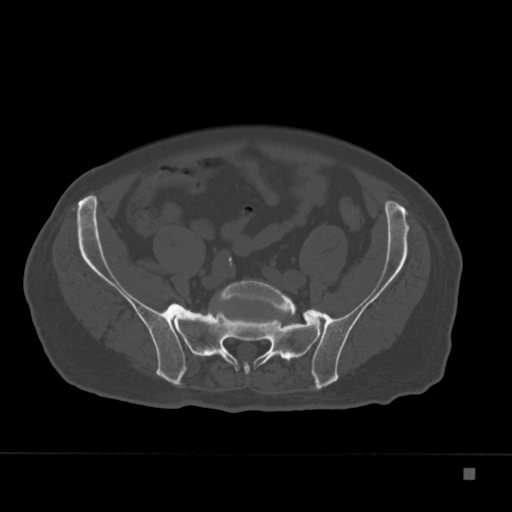
CT including the spine, one axial slice; position 9 of 332 along the scan axis; reconstruction kernel Br40s; 120 kVp; bone window (W 1800 / L 400 HU); 512 × 512 image matrix, field of view 389 × 389 mm. Patient: male, 72 years. From the clinical record (not read from this slice): primary cancer: skeletal.
Structures marked on this image (semi-automatically segmented with operator editing):
- L5 vertebra: bounding box (x1, y1, x2, y2) in pixels: (221, 280, 295, 315)